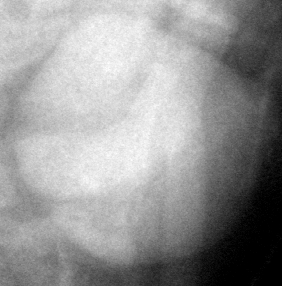
Cropped region of a digitized screen-film mammogram centred on a radiologist-marked abnormality, left breast, CC view, BI-RADS breast density category 3 (scale 1–4).
Marked abnormality: mass, shape oval, margins circumscribed; BI-RADS assessment category 3; subtlety rating 5 on a 1 (subtle) to 5 (obvious) scale; pathology result (as recorded, not read from the image): benign.